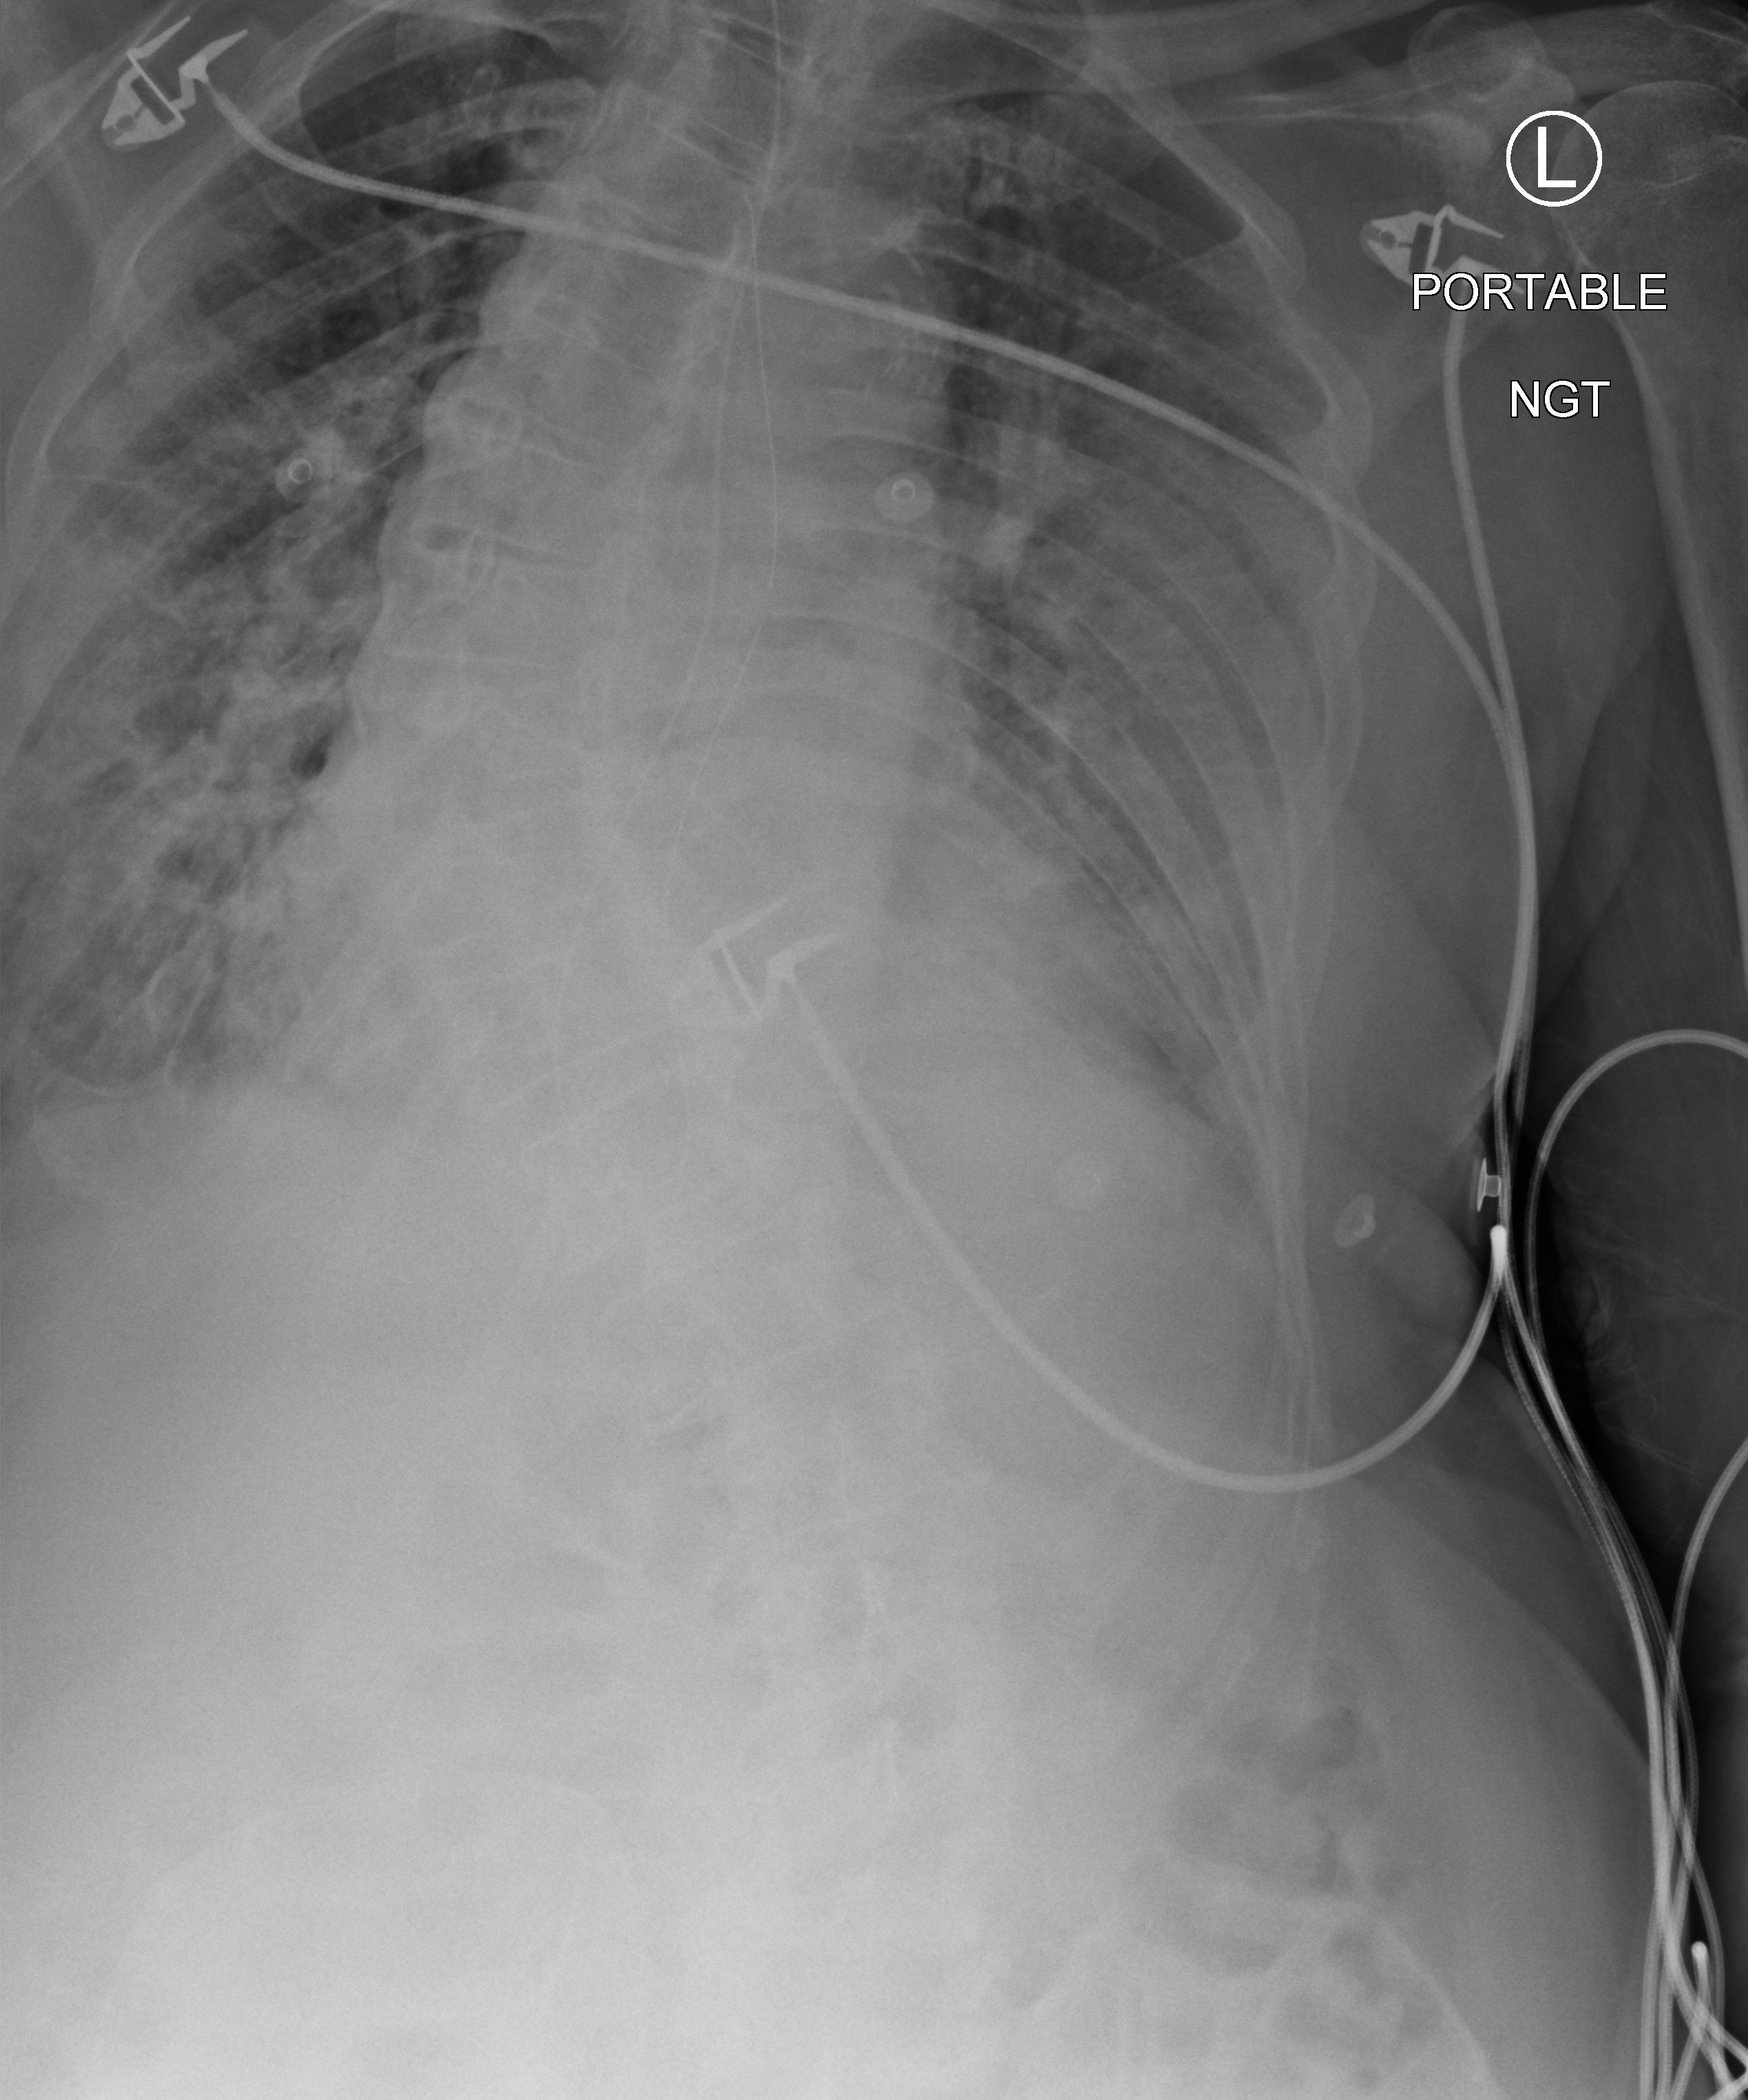
Portable chest radiograph, anteroposterior (AP) projection. Male patient hospitalised with COVID-19, age 75–90 years.
Hospital-stay facts (about this admission, not read from this image; timing relative to this image not recorded):
- mechanically ventilated during this hospital stay: no
- admitted to intensive care during this hospital stay: no